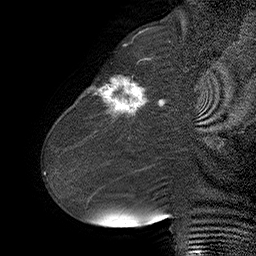
Breast MRI (dynamic contrast-enhanced), one sagittal slice; slice 21 of 55 in the series (ordered by position); dynamic contrast-enhanced series, time point 2 of 6 at this slice position (early post-contrast); 1.5 T; TE 4.5 ms, TR 32.4 ms; 256 × 256 image matrix. Female patient. From the clinical record (not read from this slice): setting: breast cancer imaged before/during neoadjuvant chemotherapy; receptor status: HER2-positive.
Structures marked on this image (semi-automatic segmentation, software-assisted and operator-edited):
- analysis volume of interest (the breast-tissue region the enhancement analysis was run in; not a lesion): box from (x=80, y=64) to (x=163, y=134) px
- tumour enhancement mask (voxels above the 100 % enhancement threshold inside the analysis volume of interest): (x=88, y=78)–(x=163, y=117)